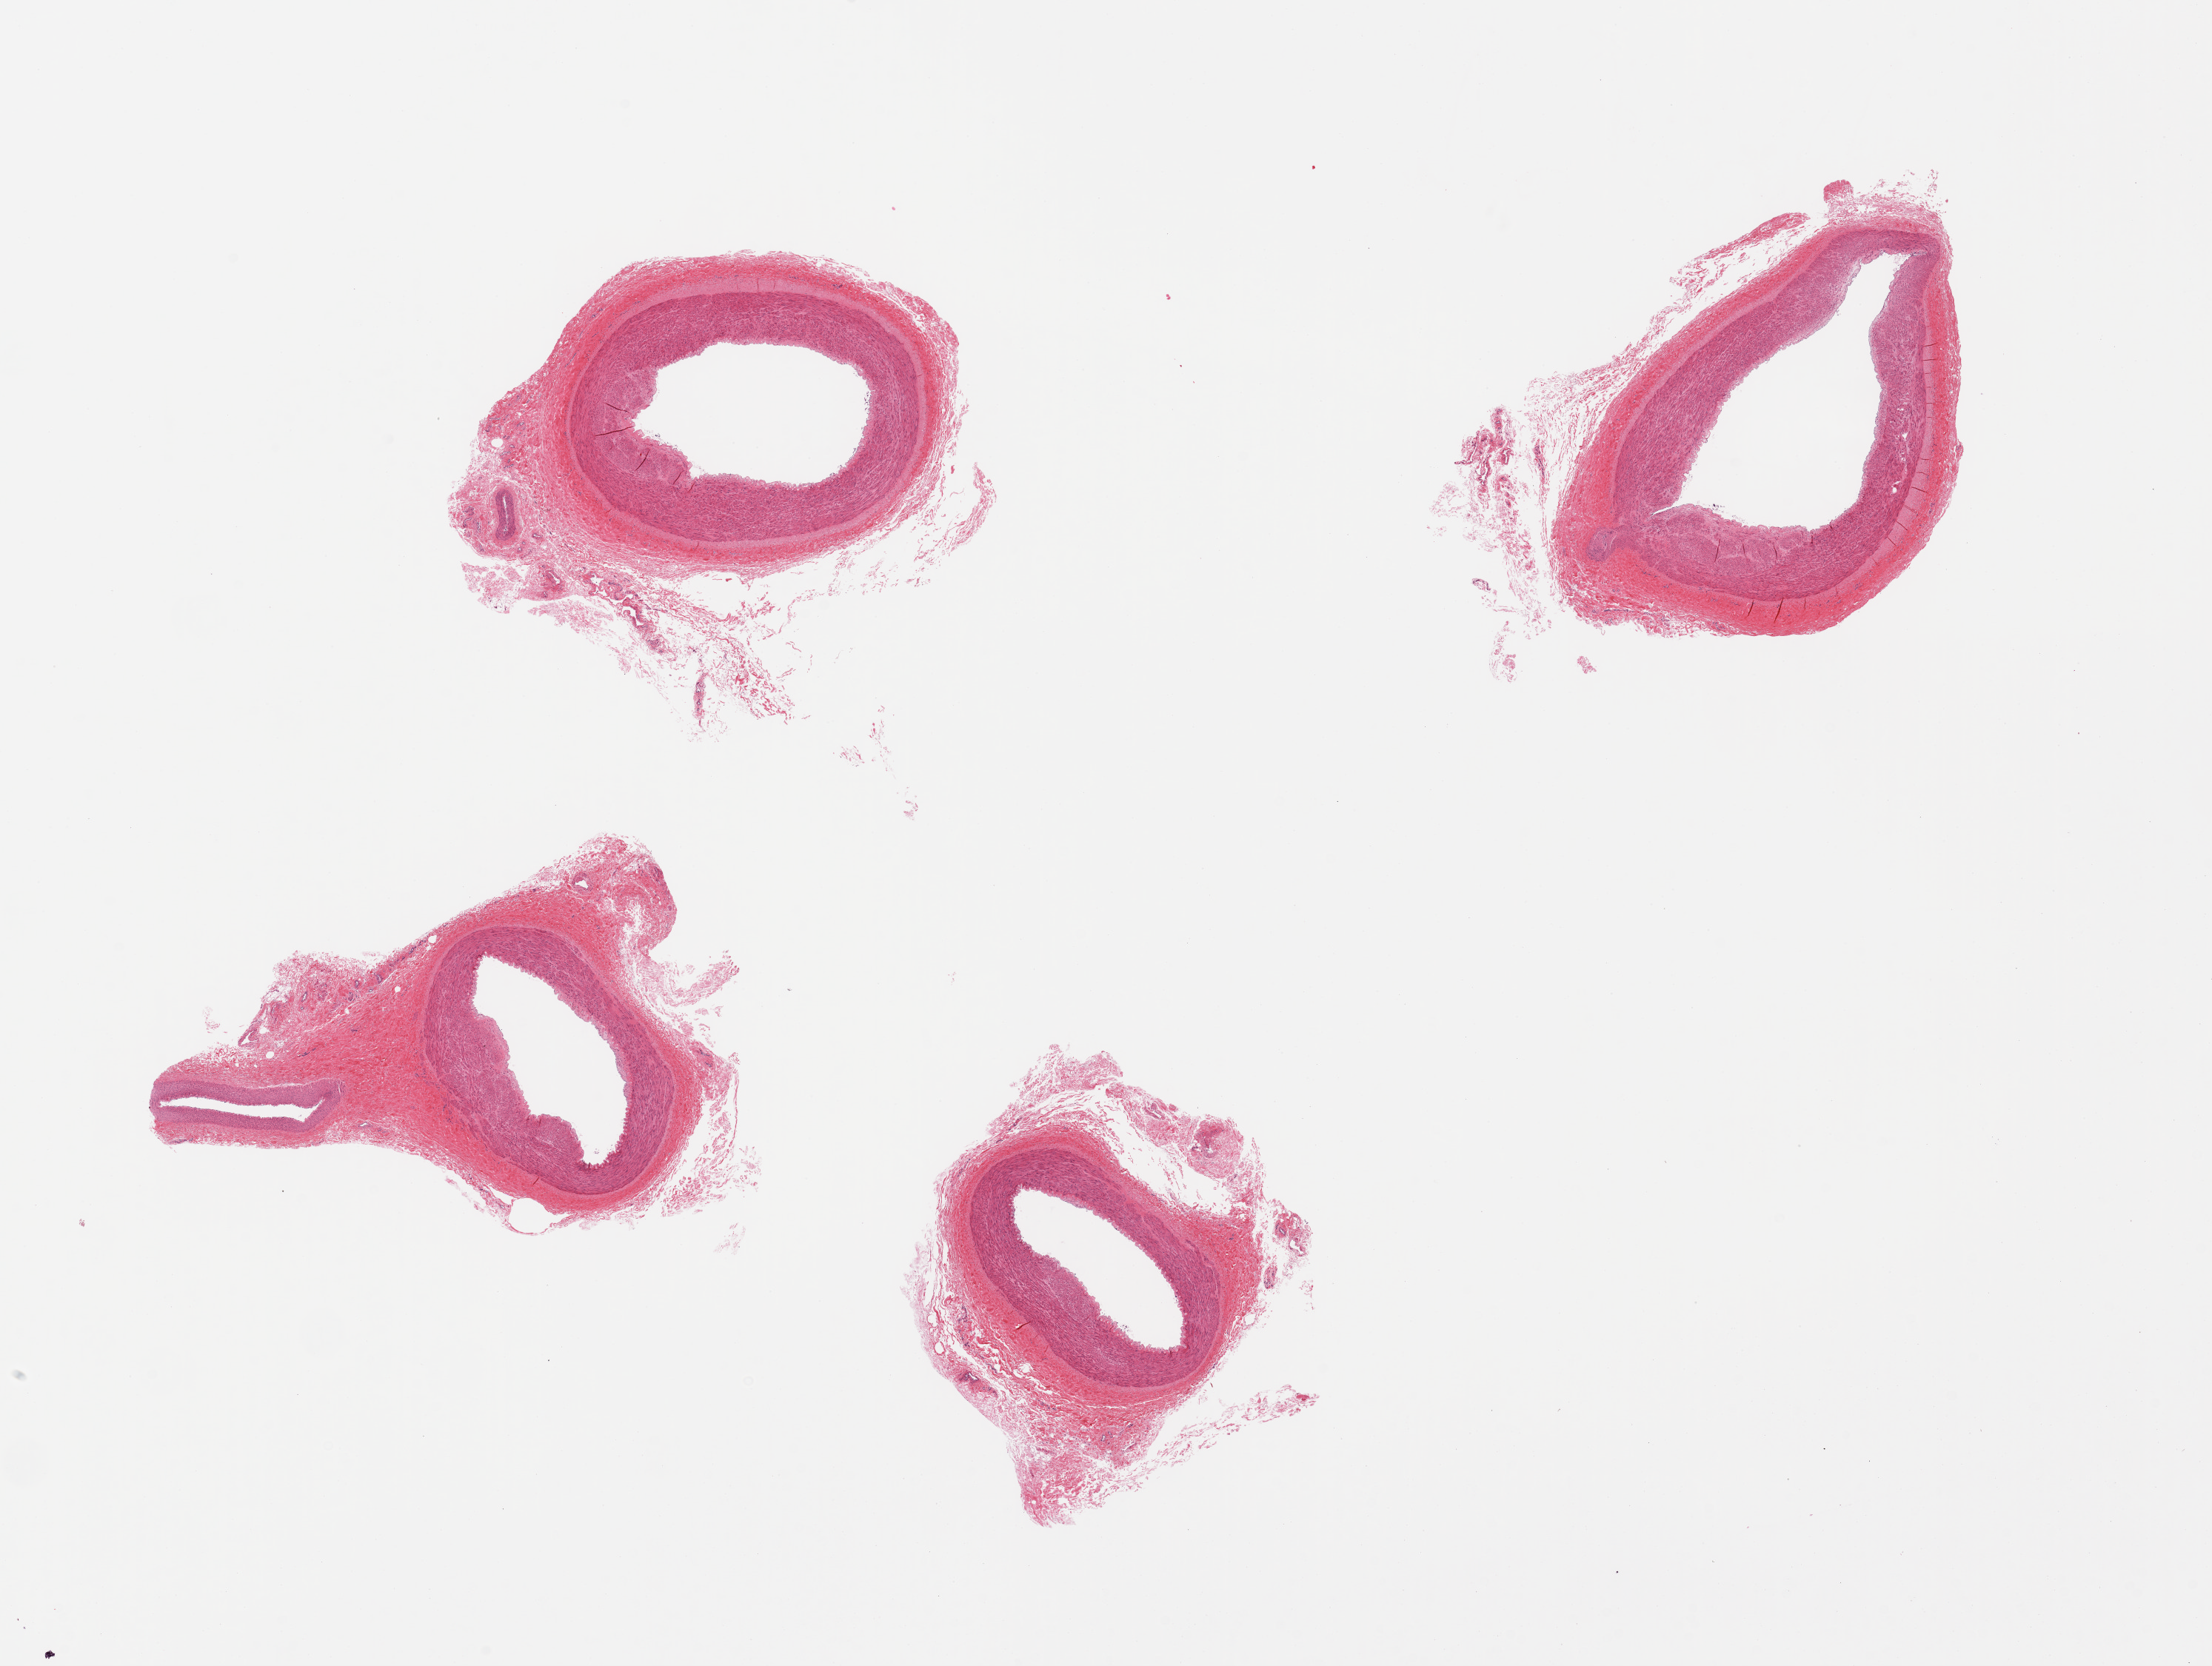
Whole-slide image, H&E stain, a low-resolution overview of the entire scanned area, about 23.6 x 17.8 mm. PAXgene-fixed paraffin-embedded (PFPE) section. Sampled site (target tissue): tibial artery. Donor tissue sample. Donor: female.
Reviewer comment on this tissue sample: 4 pieces.